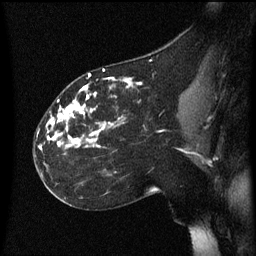
Breast MRI (dynamic contrast-enhanced), one sagittal slice; dynamic contrast-enhanced series, image 2 of 3 at this slice position (ordered by acquisition); 1.5 T; TE 4.2 ms, TR 8.4 ms; 2.2 mm slice thickness; 256 × 256 image matrix, field of view 200 × 200 mm. Female patient, age 35 years. From the clinical record (not read from this slice): setting: breast cancer imaged before/during neoadjuvant chemotherapy; receptor status: HER2-positive.
Structures marked on this image (semi-automatic segmentation, software-assisted and operator-edited):
- analysis volume of interest (the breast-tissue region the enhancement analysis was run in; not a lesion): bounding box <34,72,172,173> (left, top, right, bottom; pixels)
- tumour enhancement mask (voxels above the 70 % enhancement threshold inside the analysis volume of interest): <39,74,142,151>